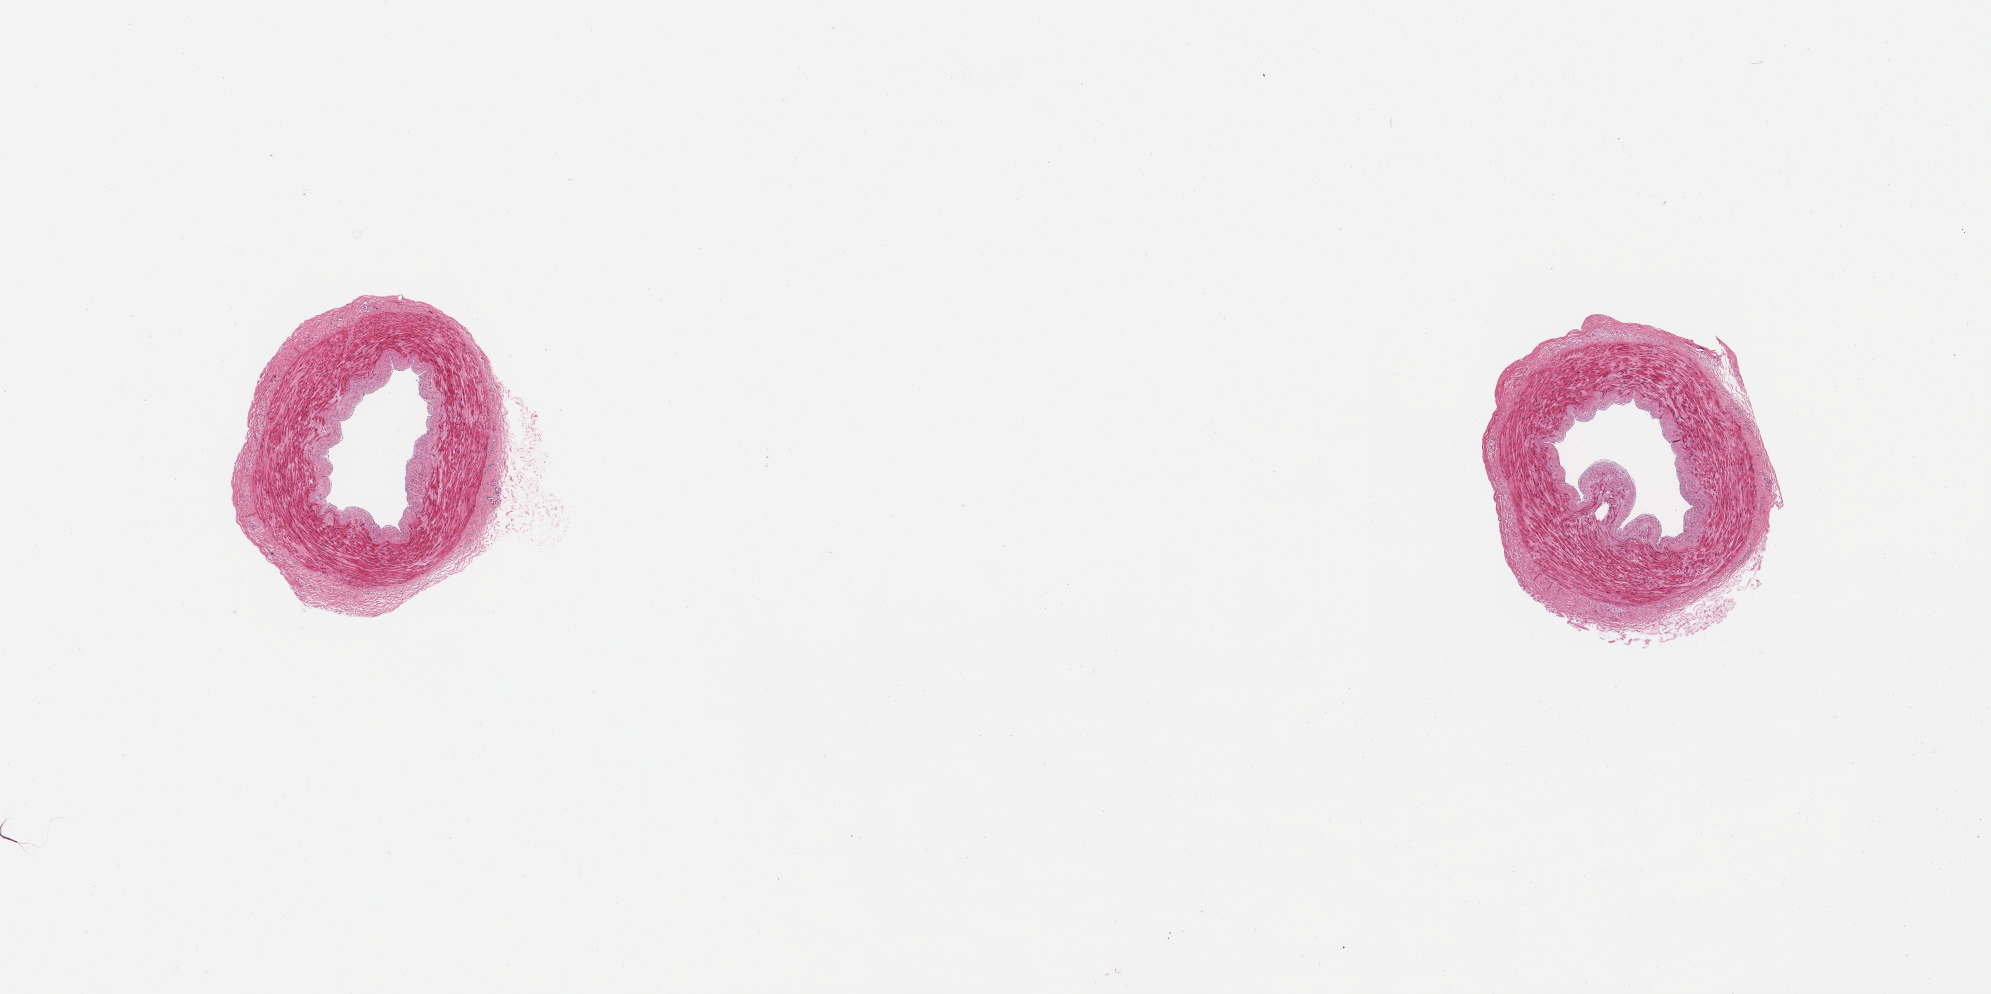
Digitized hematoxylin and eosin (H&E)-stained section, brightfield, whole scanned area (about 15.8 x 7.9 mm) shown as a low-resolution overview; PAXgene-fixed, paraffin-embedded tissue; sampled site (target tissue): tibial artery; tissue donor sample. Male donor.
- pathologist's review note for this sample: 2 pieces; no plaques; well trimmed